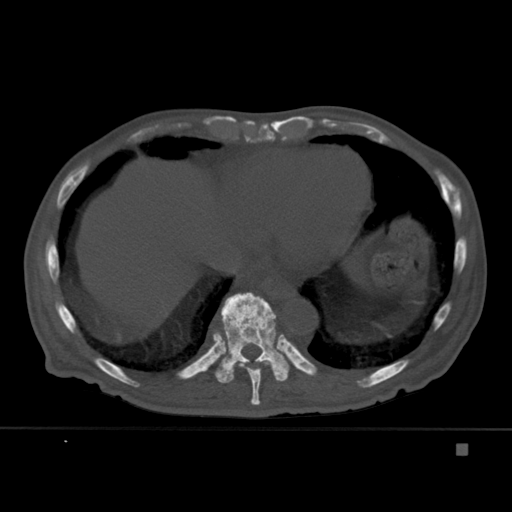
CT including the spine, one axial slice. Bone window (W 1800 / L 400 HU). 512 × 512 image matrix. Patient: male, 75 years. From the clinical record (not read from this slice): primary cancer: prostate.
Outlined on this slice (semi-automatically segmented with operator editing):
- T10 vertebra: bounding box (x1, y1, x2, y2) in pixels: (213, 292, 290, 383)
- T9 vertebra: (232, 361, 269, 405)